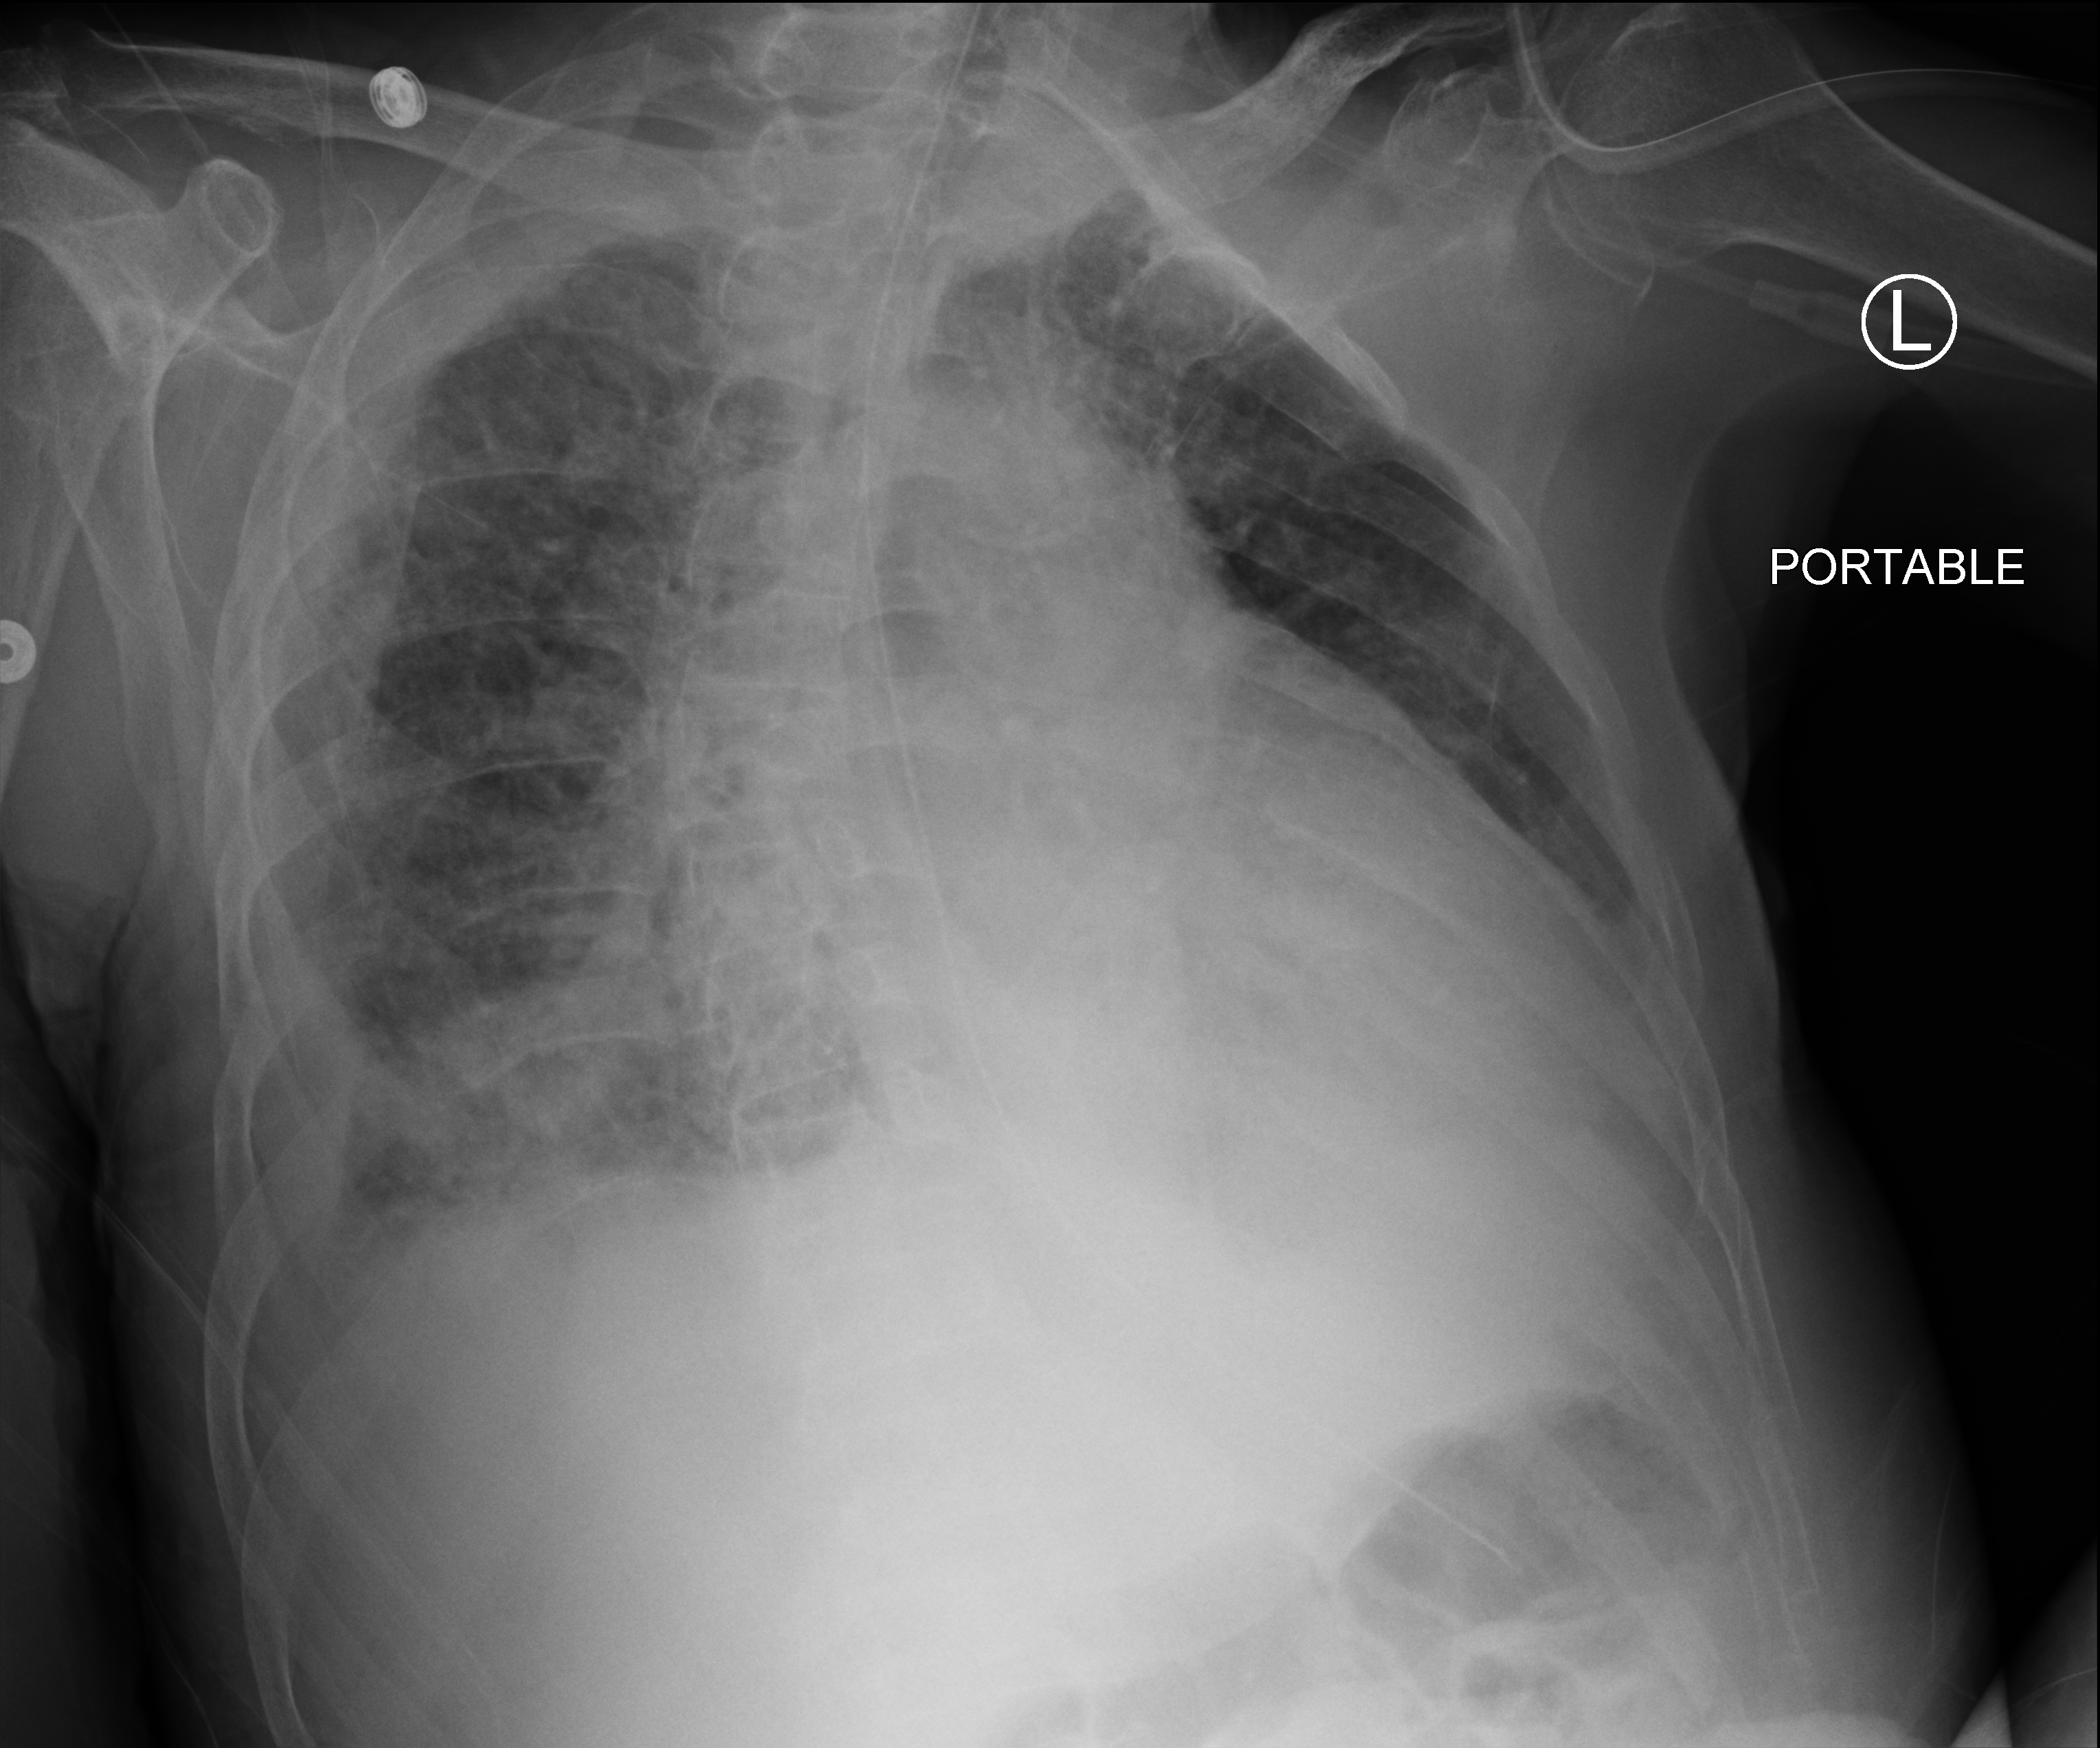
Chest X-ray (portable), anteroposterior (AP) projection. Male patient hospitalised with COVID-19, age 75–90 years.
Admission-level facts for this patient (not findings on this image; timing relative to this image not recorded):
- mechanically ventilated during this hospital stay: no